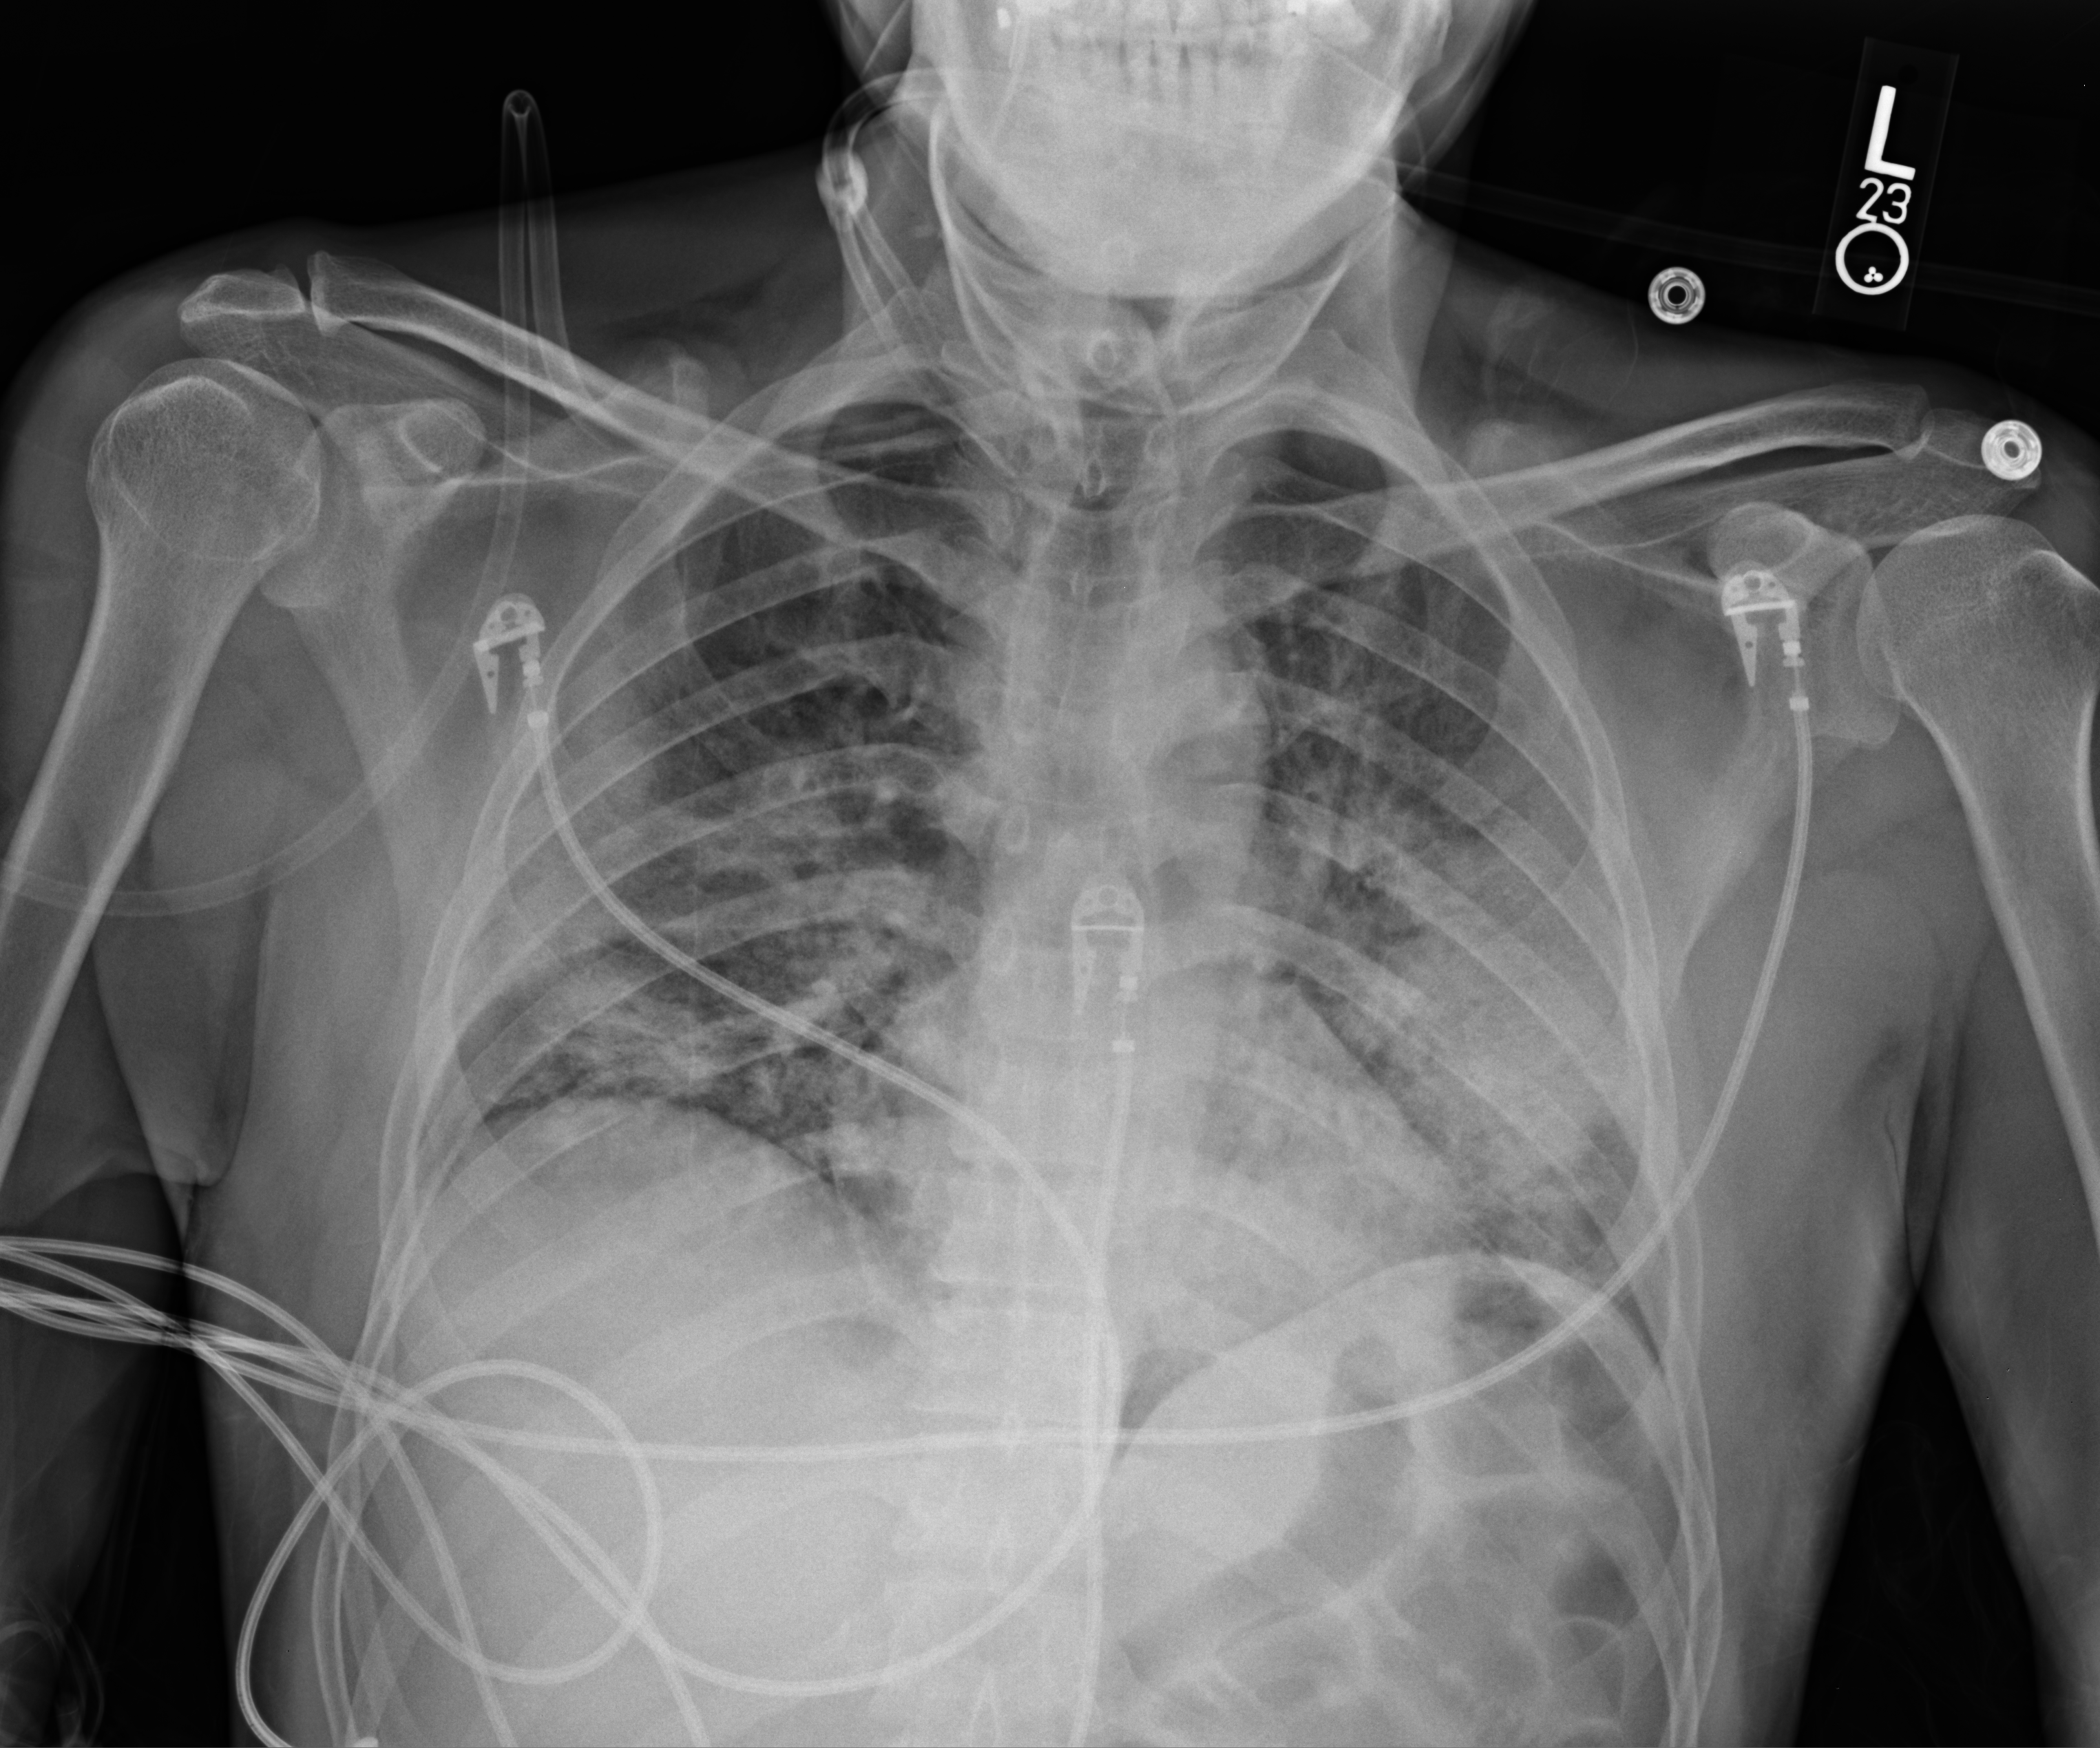
Chest X-ray (portable); anteroposterior (AP) projection. Male patient hospitalised with COVID-19, age 18–59 years.
From the hospital-stay record, not from the radiograph (when in the stay this image was taken is not recorded): mechanically ventilated during this hospital stay: no; length of hospital stay: 14 days.